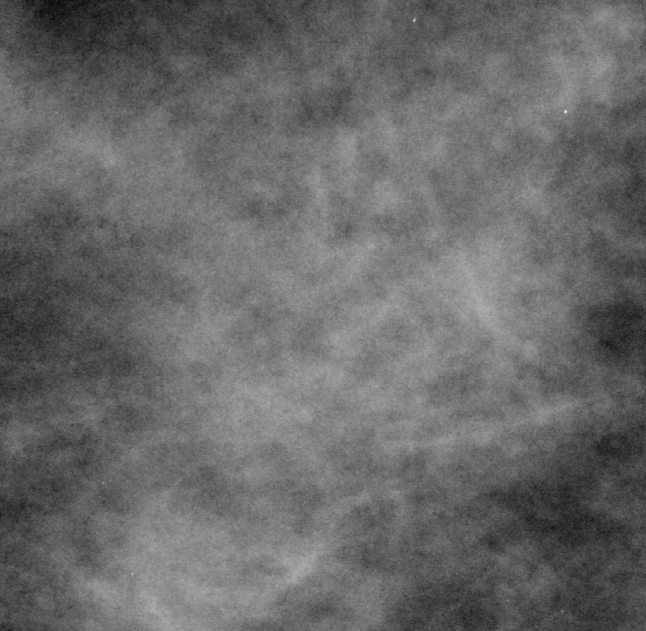
Crop from a digitized film mammogram around one marked abnormality; left breast; CC view.
- Mass, shape asymmetric breast tissue; BI-RADS assessment category 3; benign without callback (not worked up further).